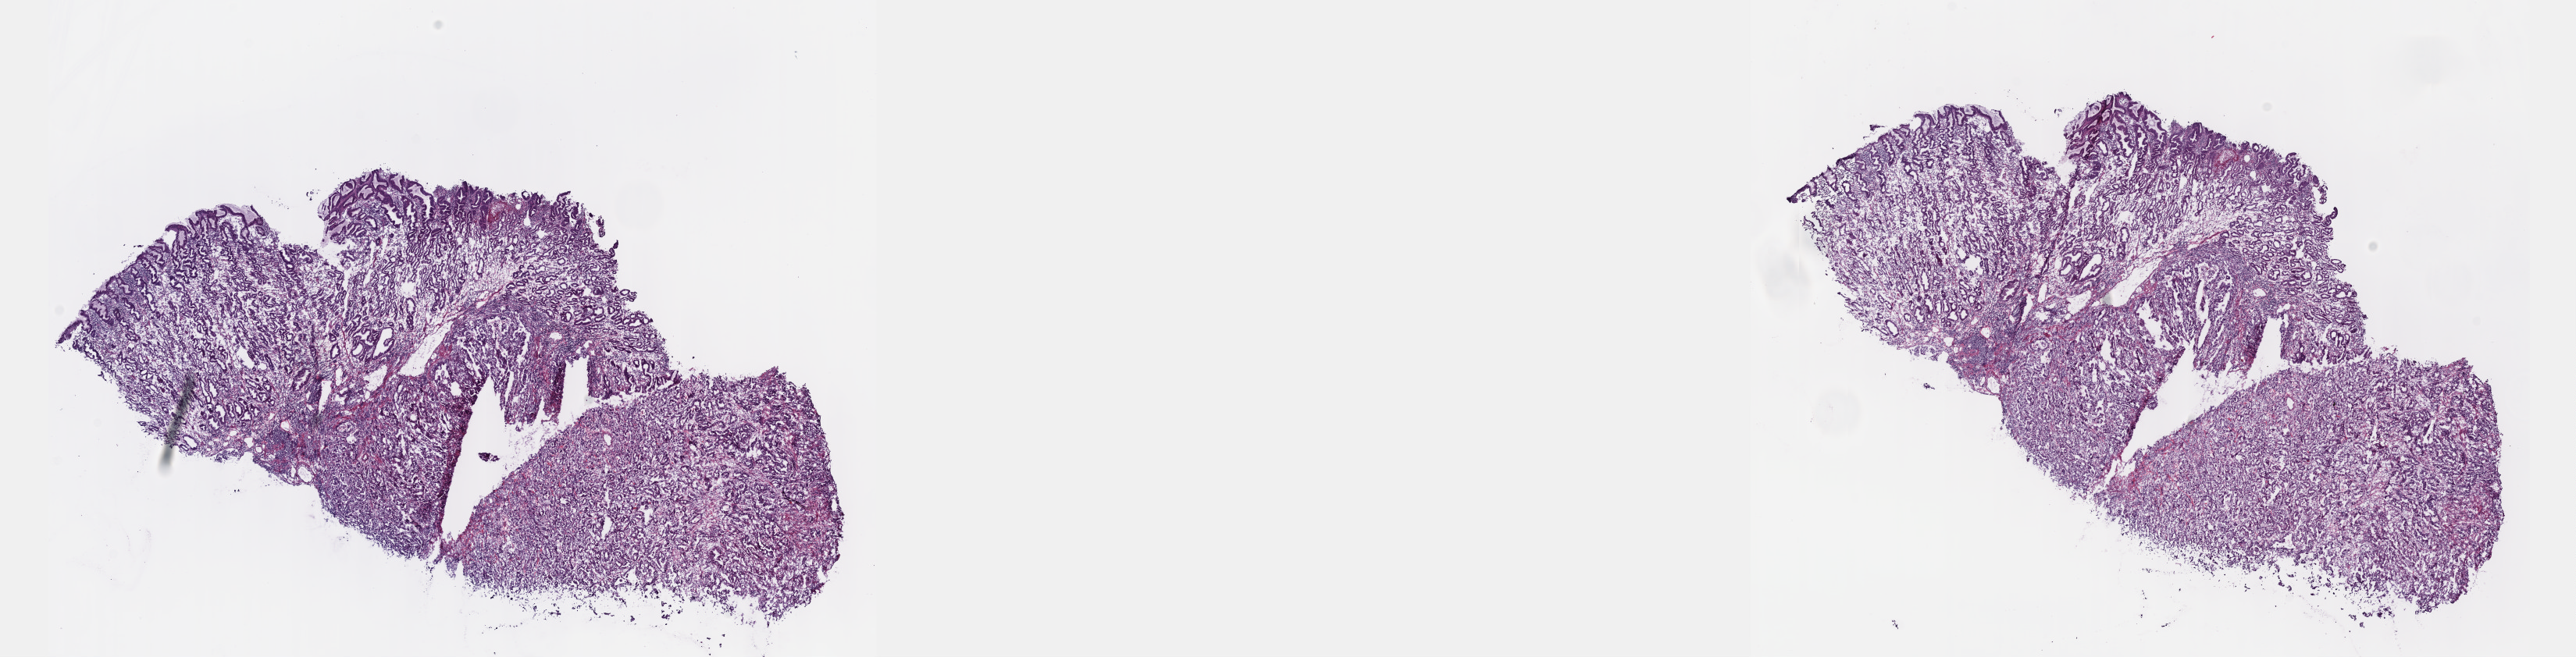
Whole-slide histology image, Hematoxylin and eosin (H&E) stained — a low-resolution overview of the entire scanned area, about 26.7 x 6.8 mm (slide scanned at 40x). Frozen section from the top of the tissue portion. Stomach, primary tumour sample. Patient: male, age at initial diagnosis 58 years. Histologic grade: G2 (moderately differentiated). Composition of this section per pathologist review: tumour cells 70%, tumour nuclei 70%, normal cells 15%, stromal cells 15%, necrosis 0%. Infiltration values recorded for this section: lymphocyte infiltration 3%, monocyte infiltration 1%, neutrophil infiltration 3%.
Diagnosis: Adenocarcinoma, intestinal type (cardia, NOS). AJCC pathologic stage: IIIB (7th edition).